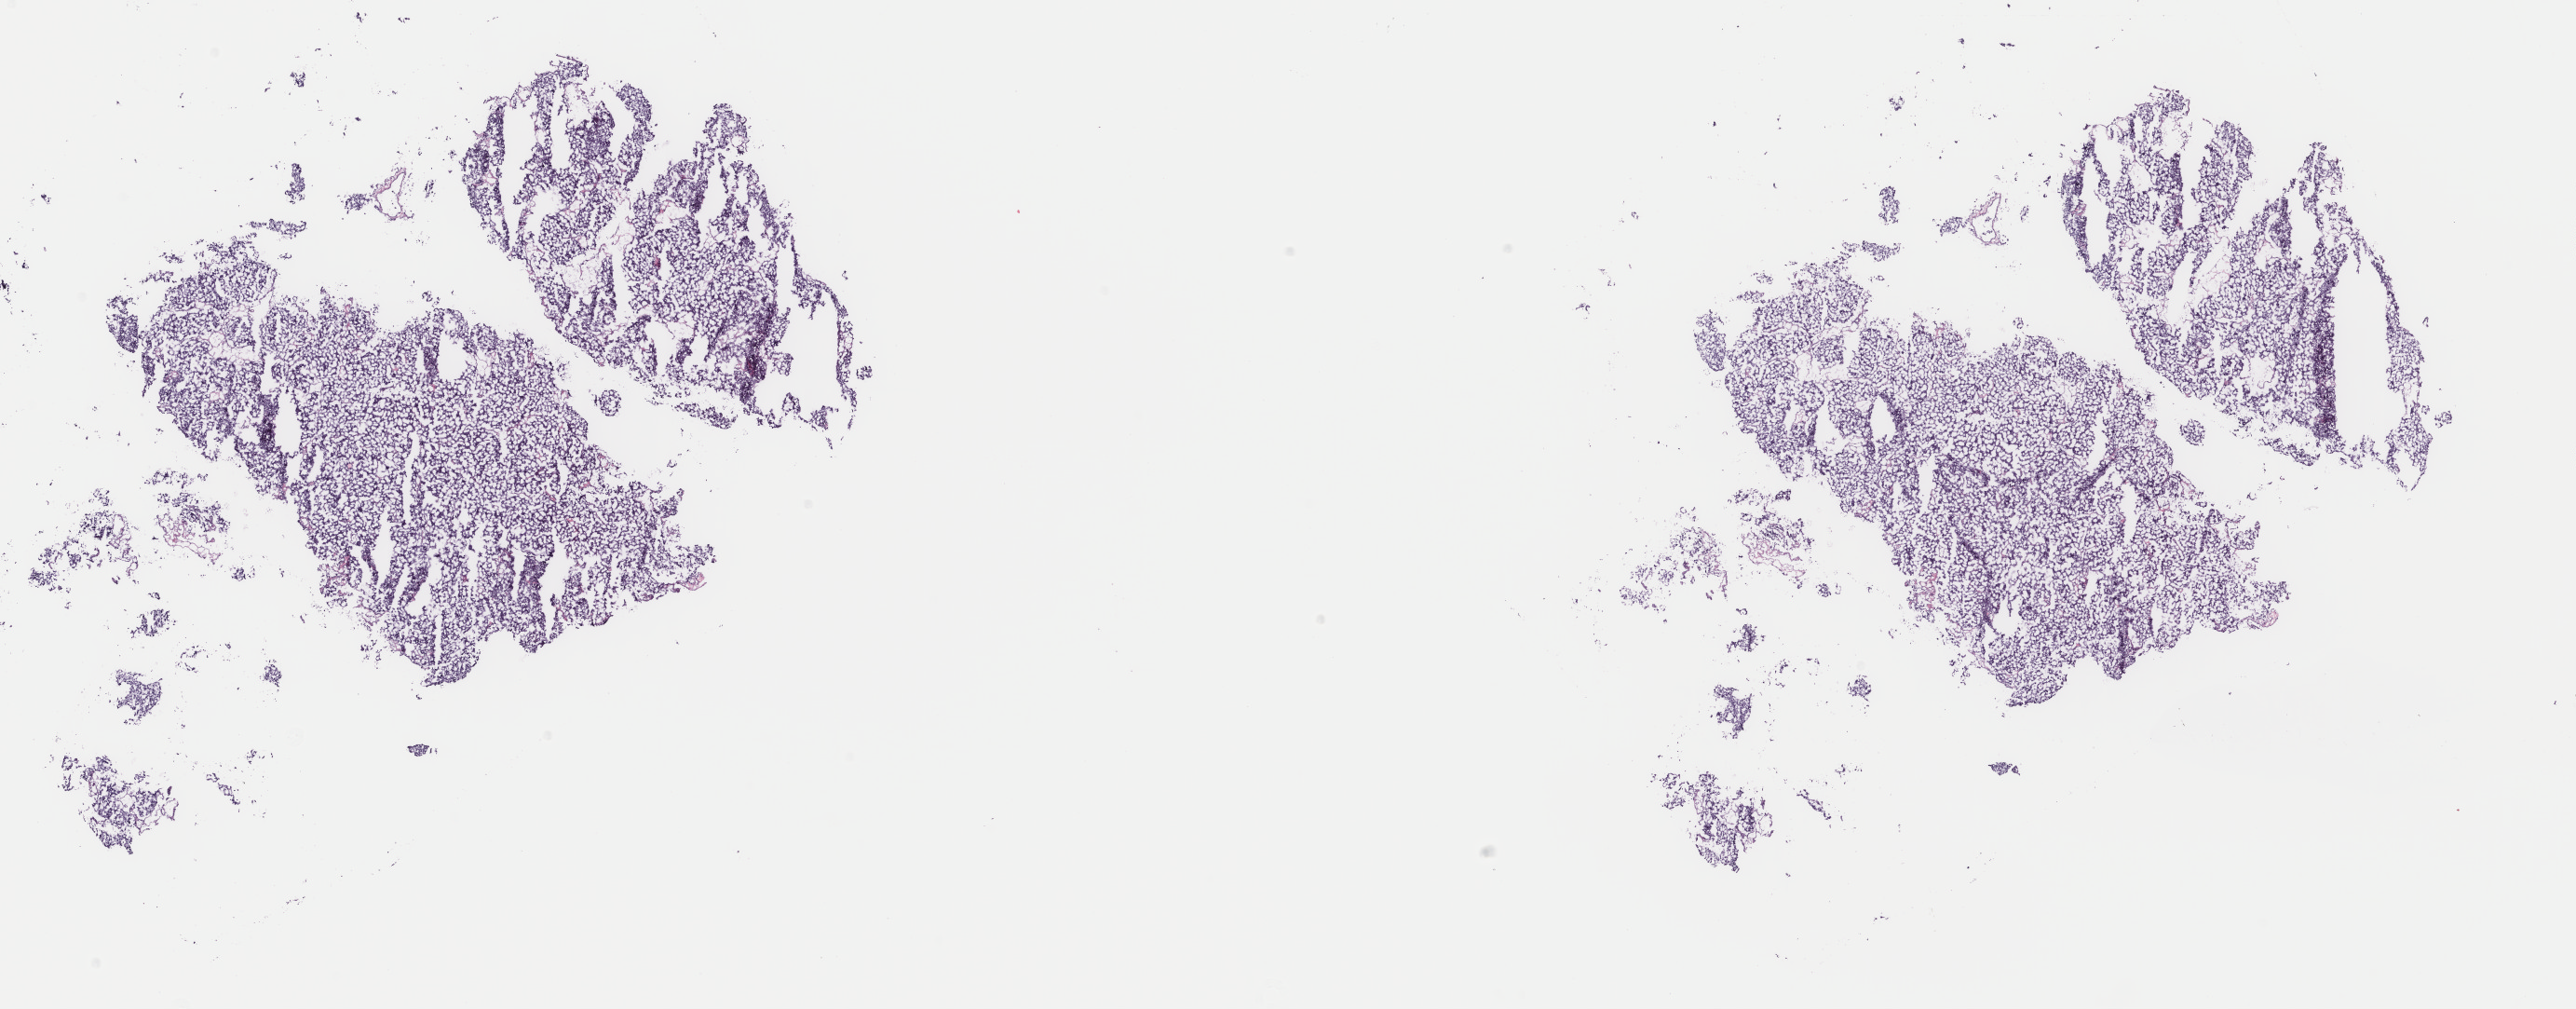
Hematoxylin and eosin (H&E) stained whole-slide image — low-resolution overview of the scanned area, about 22.0 x 8.6 mm, frozen section, adrenal gland, primary tumour sample. Patient: male, age at initial diagnosis 36 years. Slide review estimates, as recorded: tumour cells 90%, tumour nuclei 100%, normal cells 0%, stromal cells 10%, necrosis 0%. Infiltration values recorded for this section: lymphocyte infiltration 0%, monocyte infiltration 0%, neutrophil infiltration 0%.
Laterality: left. Histologic diagnosis: Pheochromocytoma, NOS.